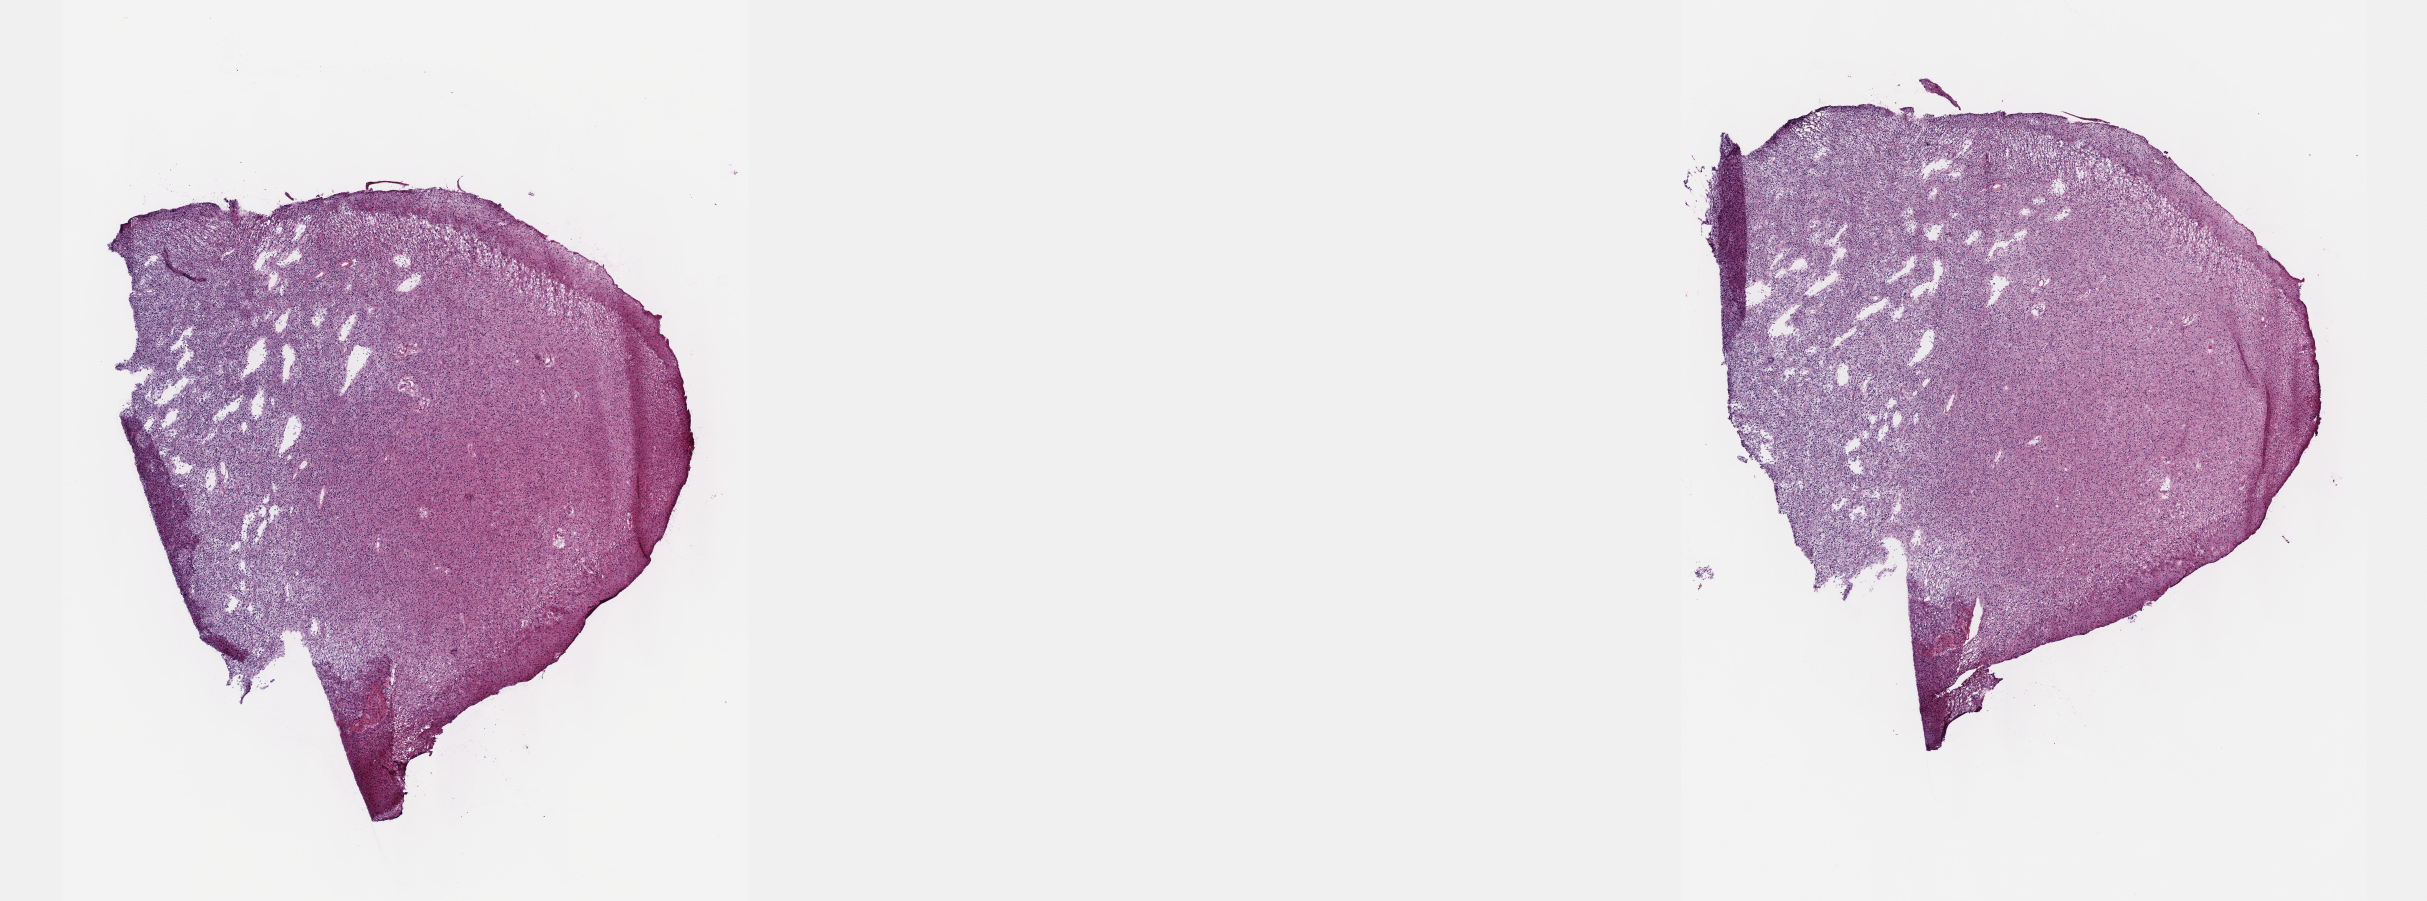
Digitized H&E-stained tissue section (whole slide), whole scanned area (about 19.6 x 7.3 mm, slide scanned at 40x) shown as a low-resolution overview. Frozen section from the top of the tissue portion. Primary tumour sample from the brain. Female, age 27 years at initial diagnosis. Histologic grade: G3 (poorly differentiated). Slide review estimates, as recorded: tumour cells 70%, tumour nuclei 90%, normal cells 10%, stromal cells 20%, necrosis 0%. Infiltration values recorded for this section: lymphocyte infiltration 0%, monocyte infiltration 0%, neutrophil infiltration 0%.
• histologic diagnosis: Oligodendroglioma, anaplastic (cerebrum)